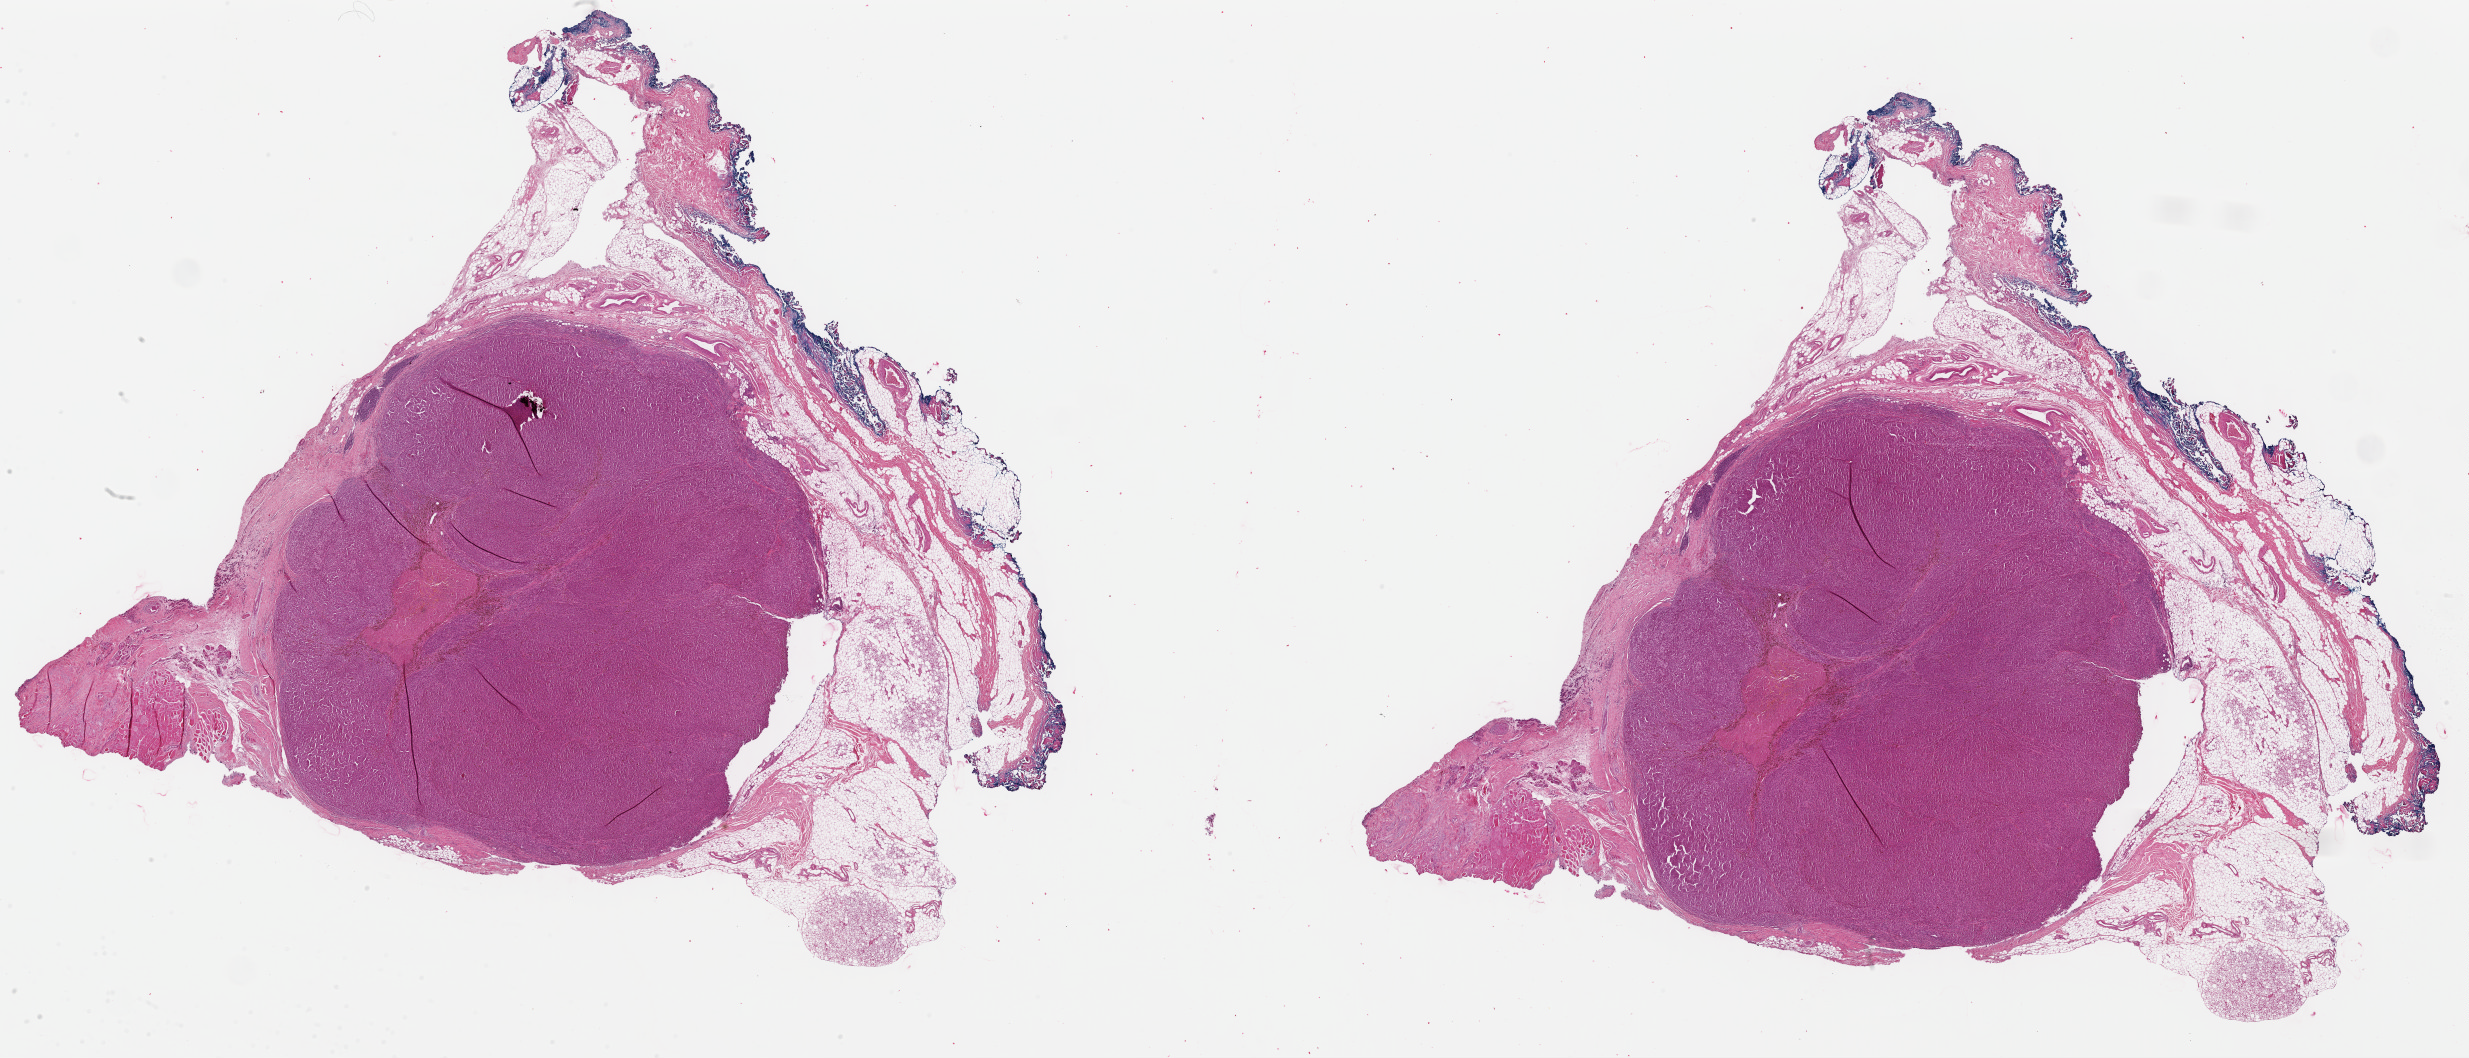
Hematoxylin and eosin (H&E) stained whole-slide image — whole scanned area (about 39.0 x 16.7 mm) shown as a low-resolution overview. Formalin-fixed paraffin-embedded (FFPE) diagnostic section. Primary tumour sample from the skin. Female, age 48 years at initial diagnosis.
TNM: T0 N3 M0. AJCC pathologic stage: IIIC (6th edition). Diagnosis: Malignant melanoma, NOS.